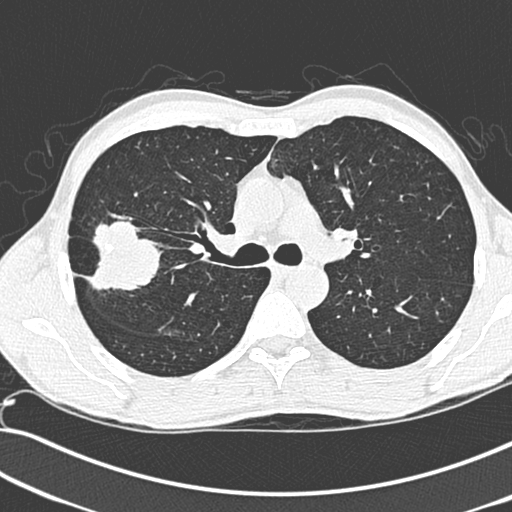
Low-dose screening chest CT, one axial slice; position 195 of 281 along the scan axis; lung window (W 1500 / L -600 HU); 512 × 512 image matrix, field of view 341 × 341 mm.
Outlined on this slice (outlined manually by an expert reader):
- lesion 1 (tumor, upper lobe of right lung): bounding box [x1, y1, x2, y2] px = [86, 220, 160, 295]